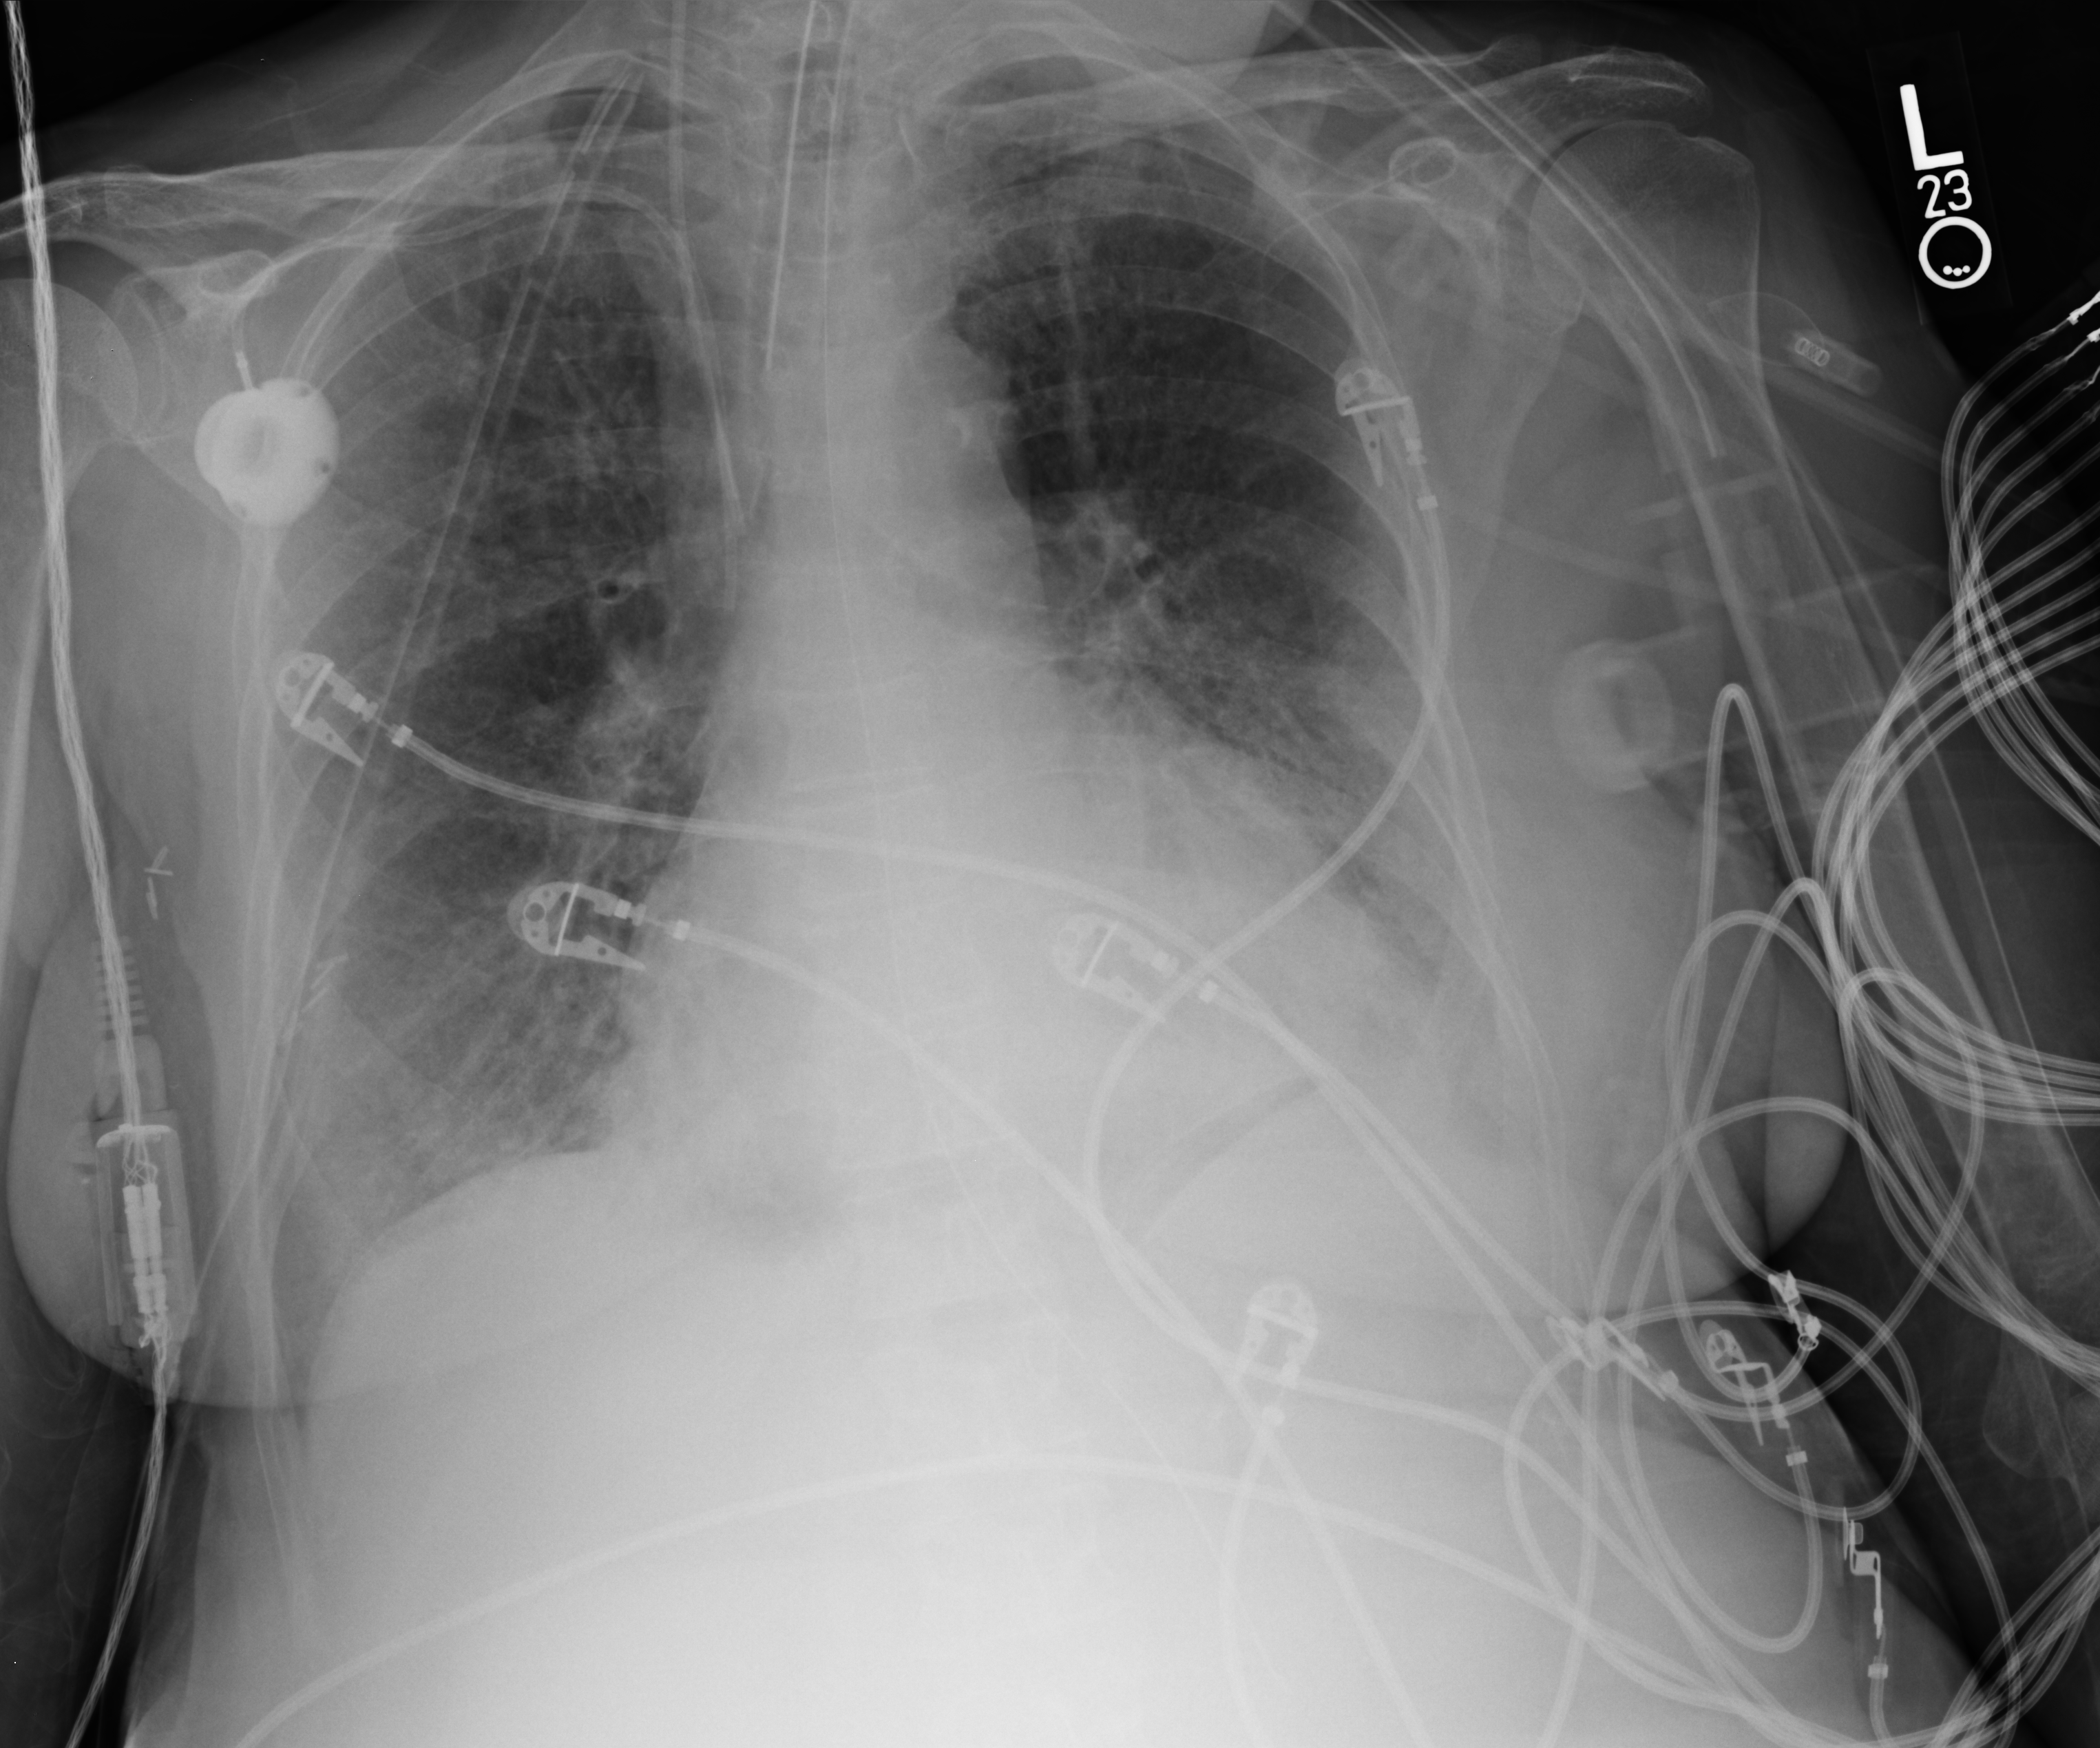
Bedside chest radiograph (computed radiography); anteroposterior (AP) projection. Patient hospitalised with COVID-19; female, aged 60–74 years.
Hospital-stay facts (about this admission, not read from this image; timing relative to this image not recorded):
- admitted to intensive care during this hospital stay: yes